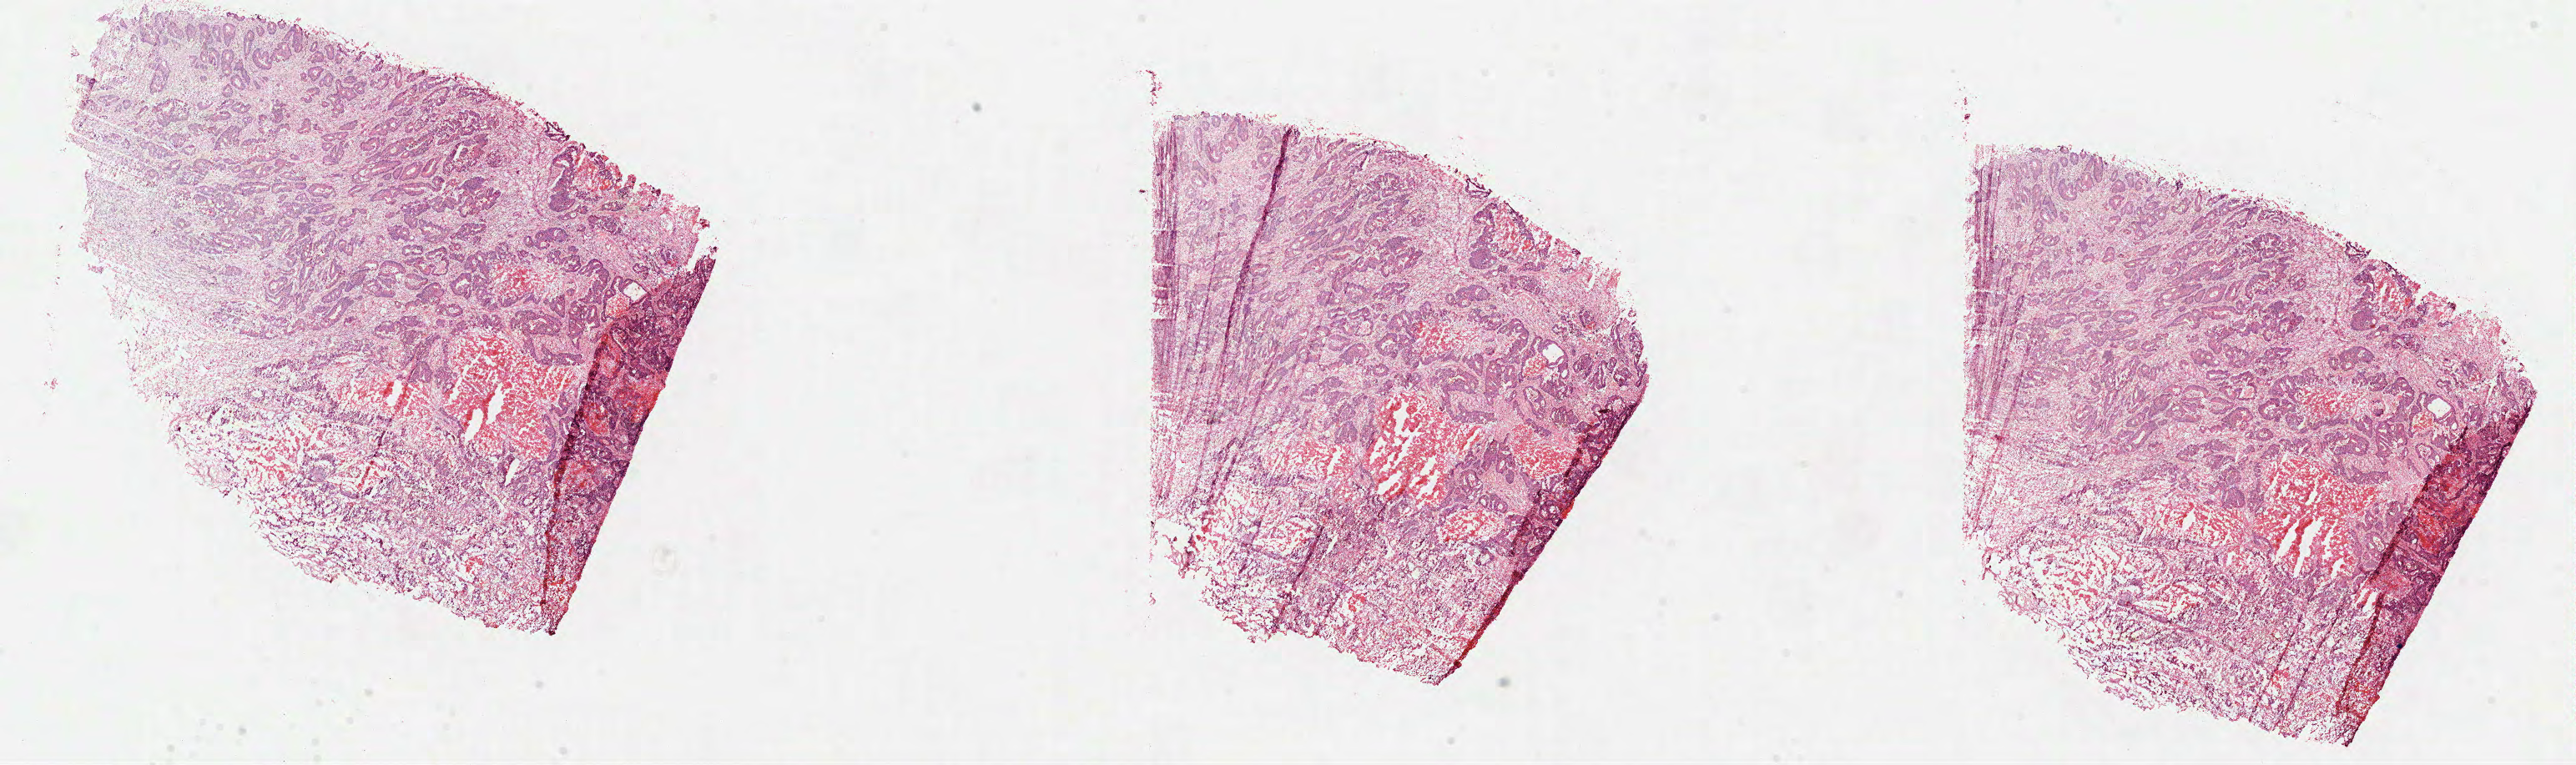
H&E whole-slide image — shown as a low-resolution overview of the whole scanned area (about 24.9 x 7.4 mm, slide scanned at 40x); formalin-fixed paraffin-embedded (FFPE) diagnostic section; primary tumour sample from the colon. Patient: male, age at initial diagnosis 69 years.
AJCC pathologic stage: IIA. Lymph nodes positive (case pathology): 0 of 11 examined. TNM: T3 N0 M0. Pathologic diagnosis: Adenocarcinoma, NOS.